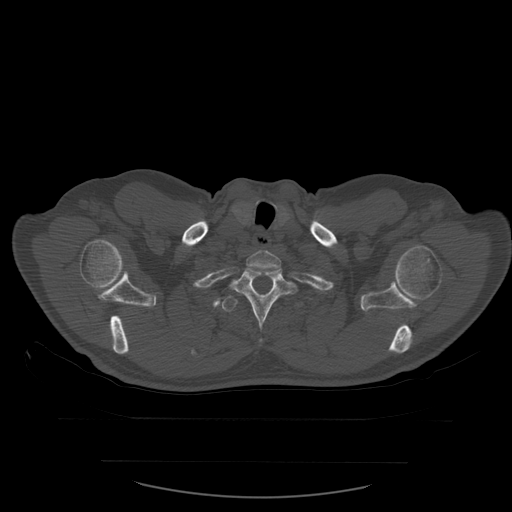
CT including the spine, one axial slice; position 475 of 590 along the scan axis; bone window (W 1800 / L 400 HU); 1.25 mm slice thickness; 512 × 512 image matrix. Patient age 71 years. From the clinical record (not read from this slice): primary cancer: lung.
Structures marked on this image (semi-automatically segmented with operator editing):
- T1 vertebra: bounding box (x1, y1, x2, y2) in pixels: (247, 251, 283, 272)
- T2 vertebra: (227, 266, 300, 341)
- T3 vertebra: (222, 295, 304, 313)